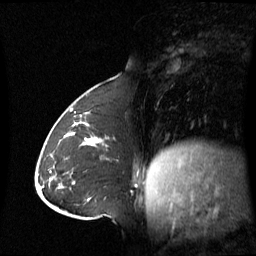
Breast MRI (dynamic contrast-enhanced), one sagittal slice; slice 25 of 60 in the series (ordered by position); dynamic contrast-enhanced series, image 2 of 3 at this slice position (ordered by acquisition); 1.5 T; TE 4.2 ms, TR 8.4 ms; 256 × 256 image matrix, field of view 270 × 270 mm. Female patient, age 43 years. From the clinical record (not read from this slice): setting: breast cancer imaged before/during neoadjuvant chemotherapy; receptor status: triple-negative.
Annotated regions visible in this slice (semi-automatic segmentation, software-assisted and operator-edited):
- analysis volume of interest (the breast-tissue region the enhancement analysis was run in; not a lesion): bounding box (x1, y1, x2, y2) in pixels: (62, 124, 137, 180)
- tumour enhancement mask (voxels above the 70 % enhancement threshold inside the analysis volume of interest): (70, 124, 100, 146)